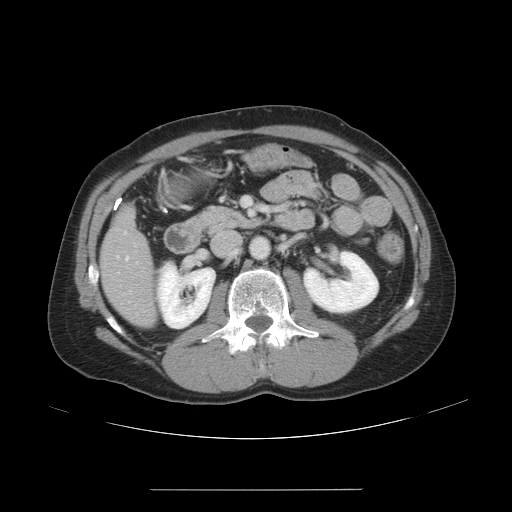
Contrast-enhanced abdominal CT, one axial slice; slice 20 of 48 in the series (ordered by position); 120 kVp; intravenous contrast given; soft-tissue window (W 400 / L 40 HU); 5 mm slice thickness; 512 × 512 image matrix, field of view 409 × 409 mm. Male patient, age 56 years. From the clinical record (not read from this slice): diagnosis: colorectal cancer liver metastases, imaged before liver resection.
Outlined on this slice (outlined manually by an expert reader):
- hepatic veins: box from (x=125, y=255) to (x=130, y=302) px
- liver: (x=102, y=210)–(x=155, y=327)
- planned liver remnant (the part of the liver to remain after resection): (x=104, y=269)–(x=155, y=327)